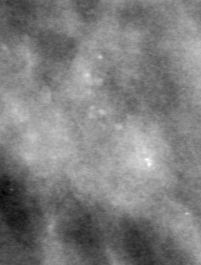
Crop from a digitized film mammogram around one marked abnormality; right breast; MLO view.
Finding: calcifications, morphology pleomorphic, distribution clustered; BI-RADS assessment category 4; subtlety rating 2 on a 1 (subtle) to 5 (obvious) scale; pathology result (as recorded, not read from the image): malignant.